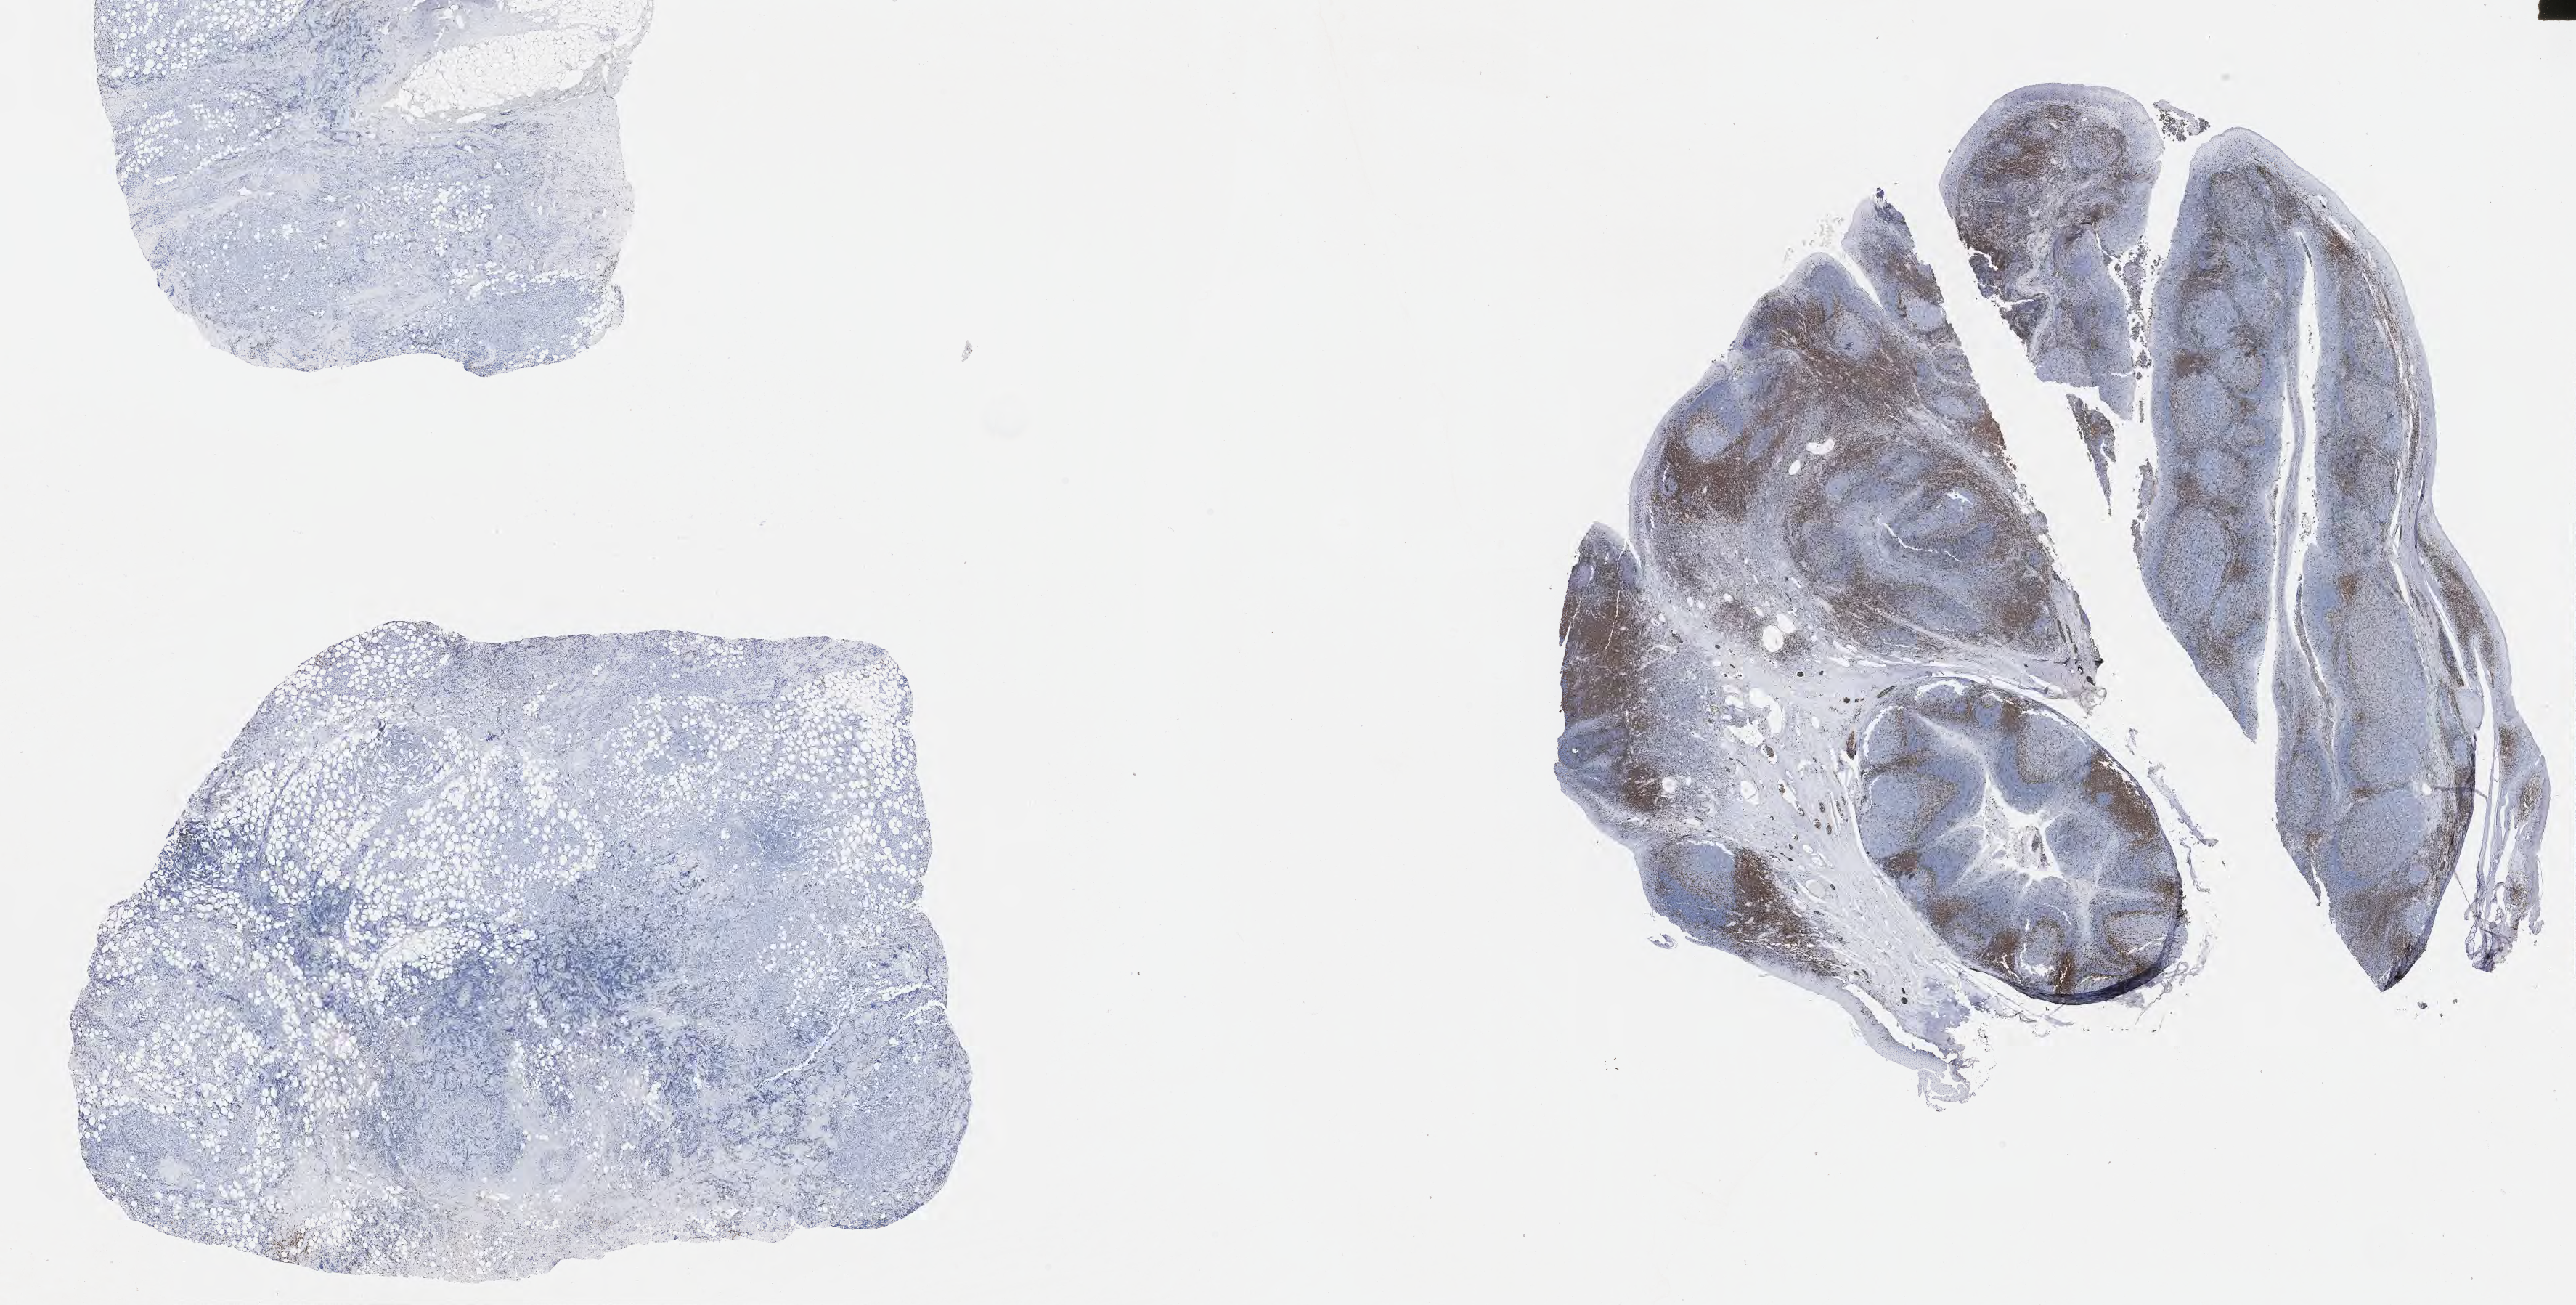
IHC for CD3, whole-slide image — low-resolution overview of the scanned area, about 28.7 x 14.5 mm, specimen: tumor tissue, site: kidney. Male patient, aged 63.
Histologic diagnosis: Diffuse large B-cell lymphoma, NOS.